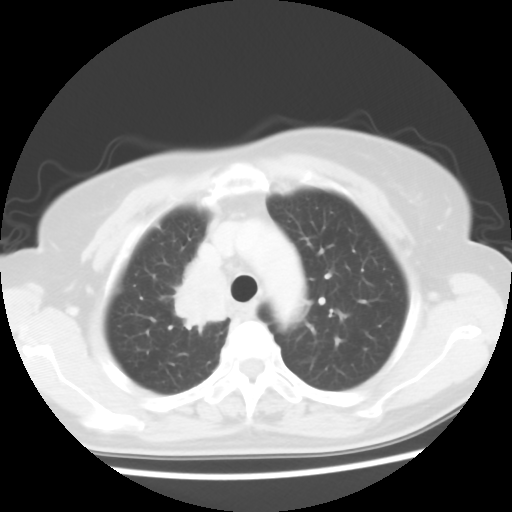
Chest CT, one axial slice. Position 44 of 56 along the scan axis. Reconstruction kernel STANDARD. 120 kVp. Lung window (W 1500 / L -600 HU). 5 mm slice thickness. 512 × 512 image matrix. Patient: female, 62 years. Case-level facts recorded for this patient, not image findings: clinical TNM (as recorded): T2 N1 M1a.
Outlined on this slice (rectangle marked by the reading radiologist):
- lung tumour (recorded histology: adenocarcinoma): bounding box <168,250,245,336> (left, top, right, bottom; pixels)